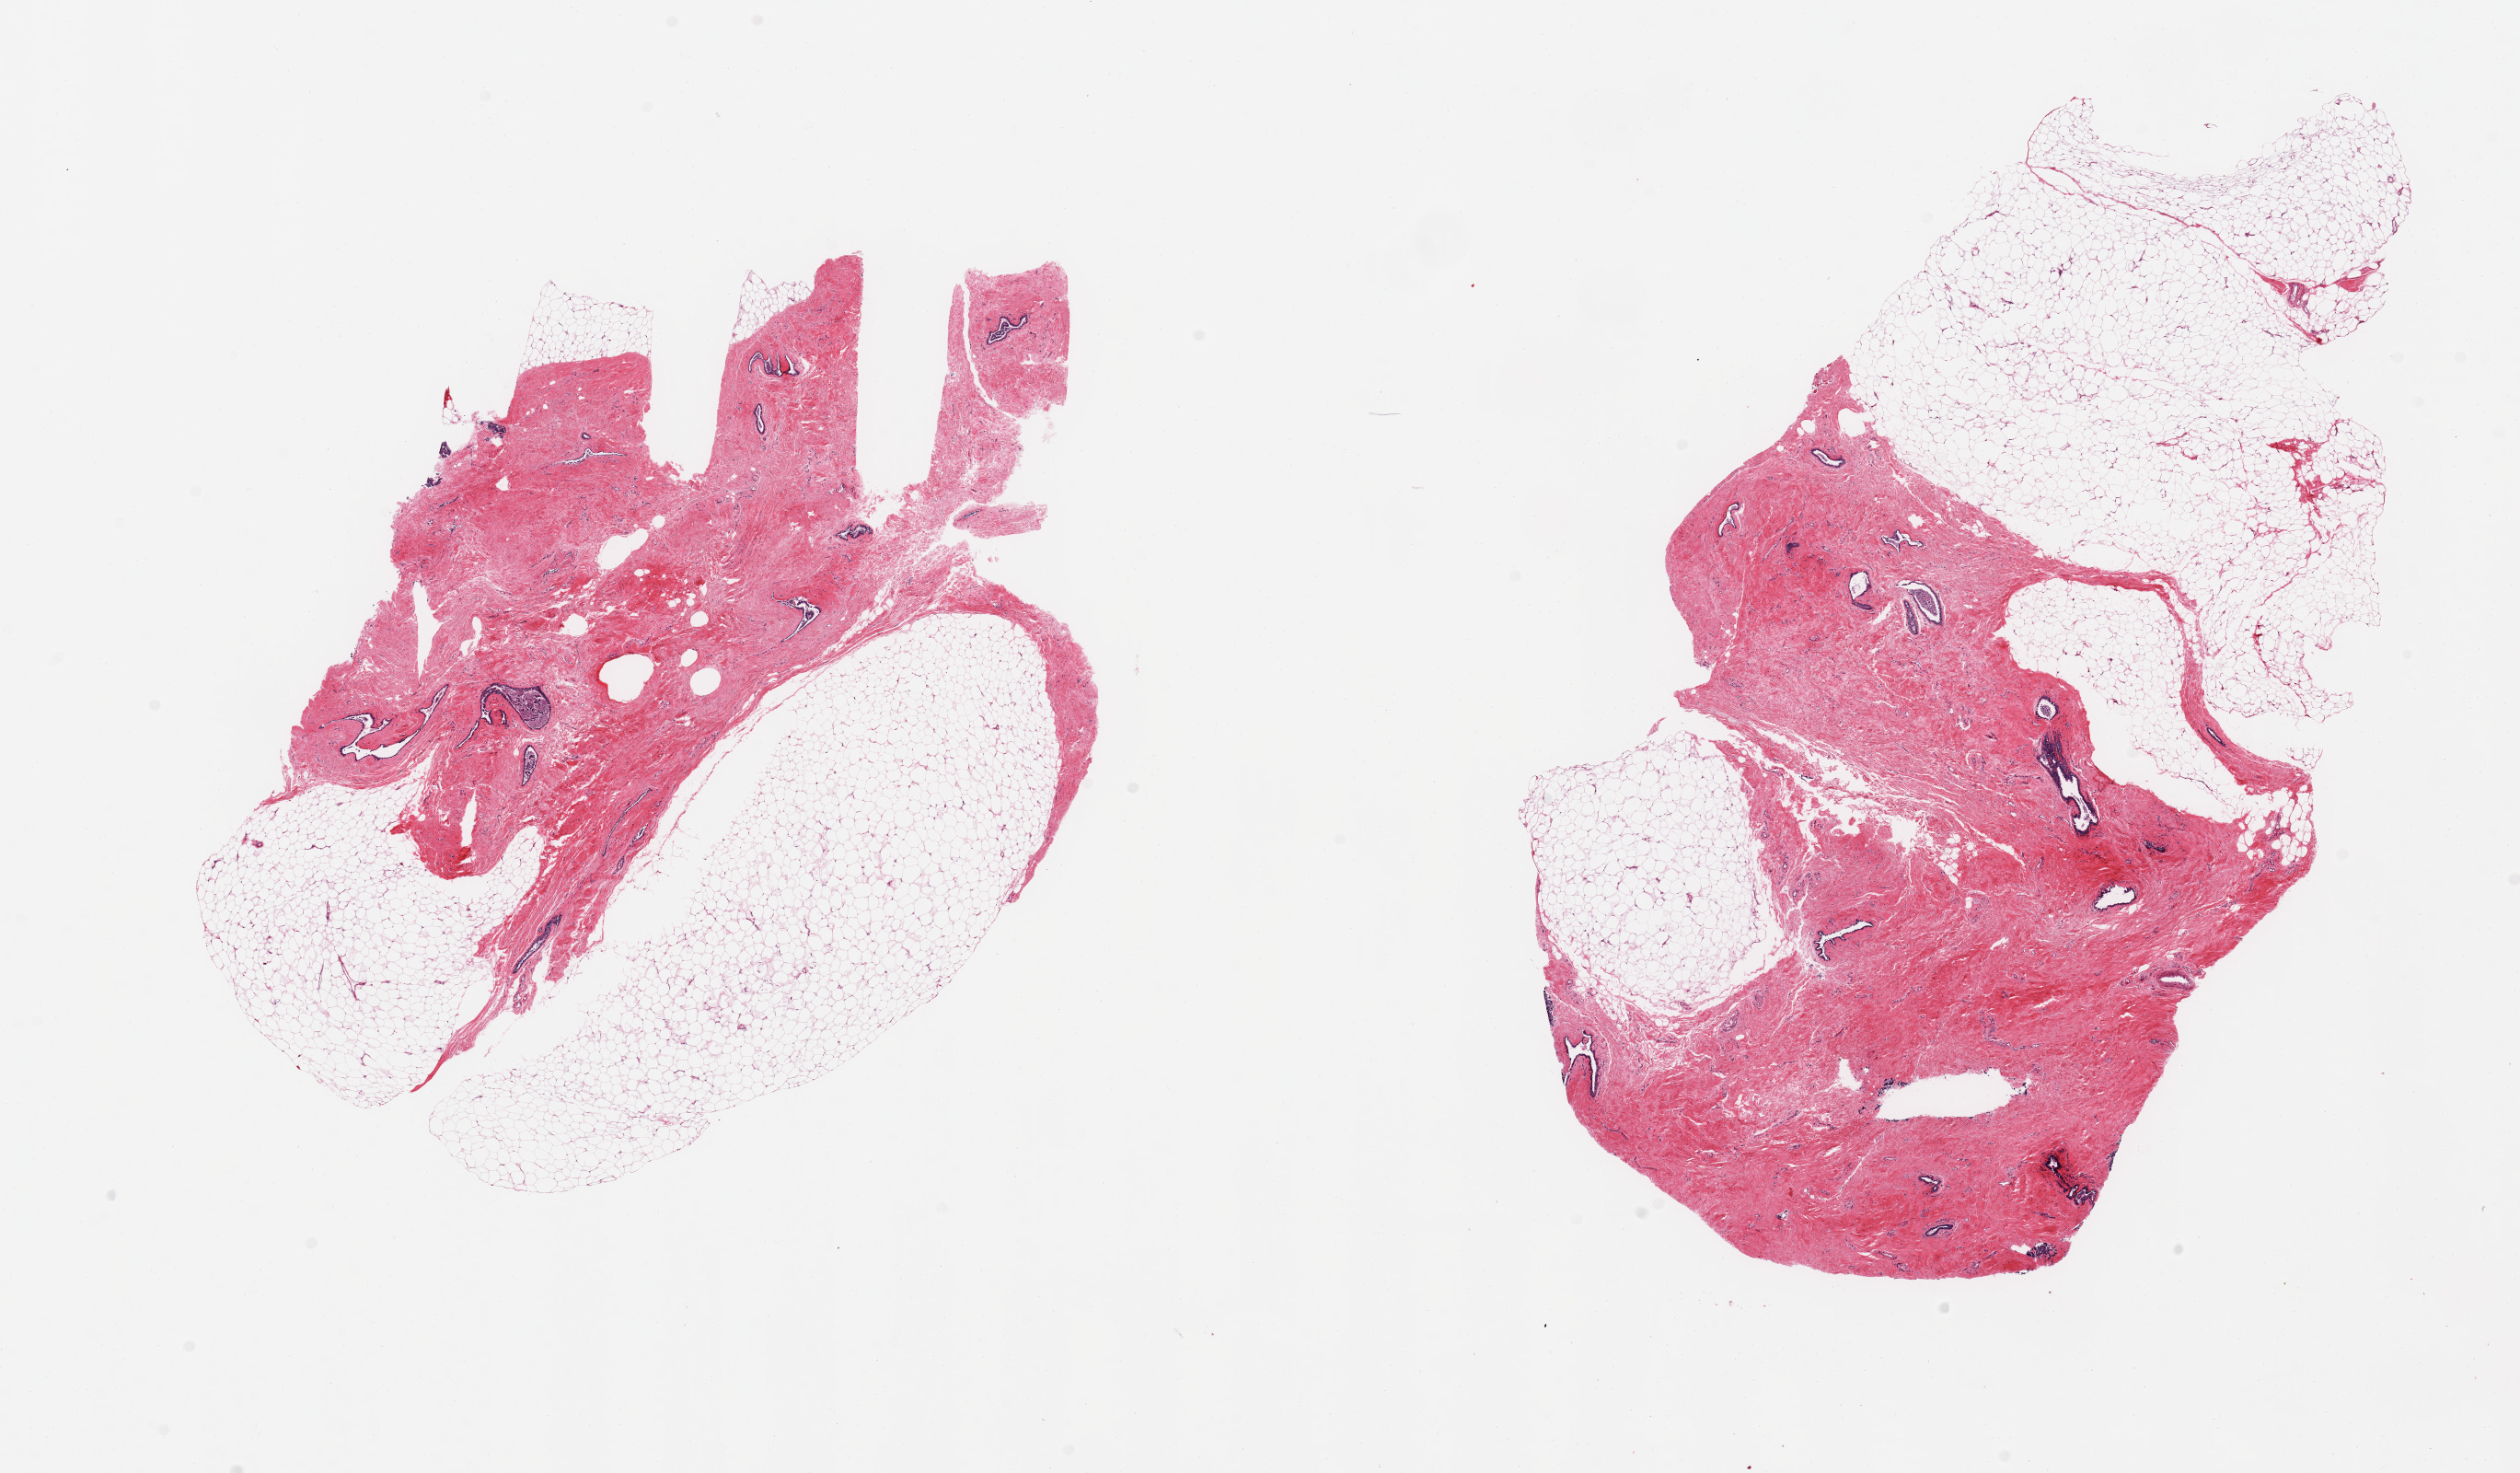
H&E whole-slide image — low-resolution overview of the scanned area, about 21.7 x 12.7 mm (acquisition: 20x scan); PAXgene-fixed, paraffin-embedded tissue; section of breast (target tissue); donor tissue sample. Donor sex: male.
Pathologist's review note for this sample: 2 pieces; fibroadipose tissue with mammary ducts.